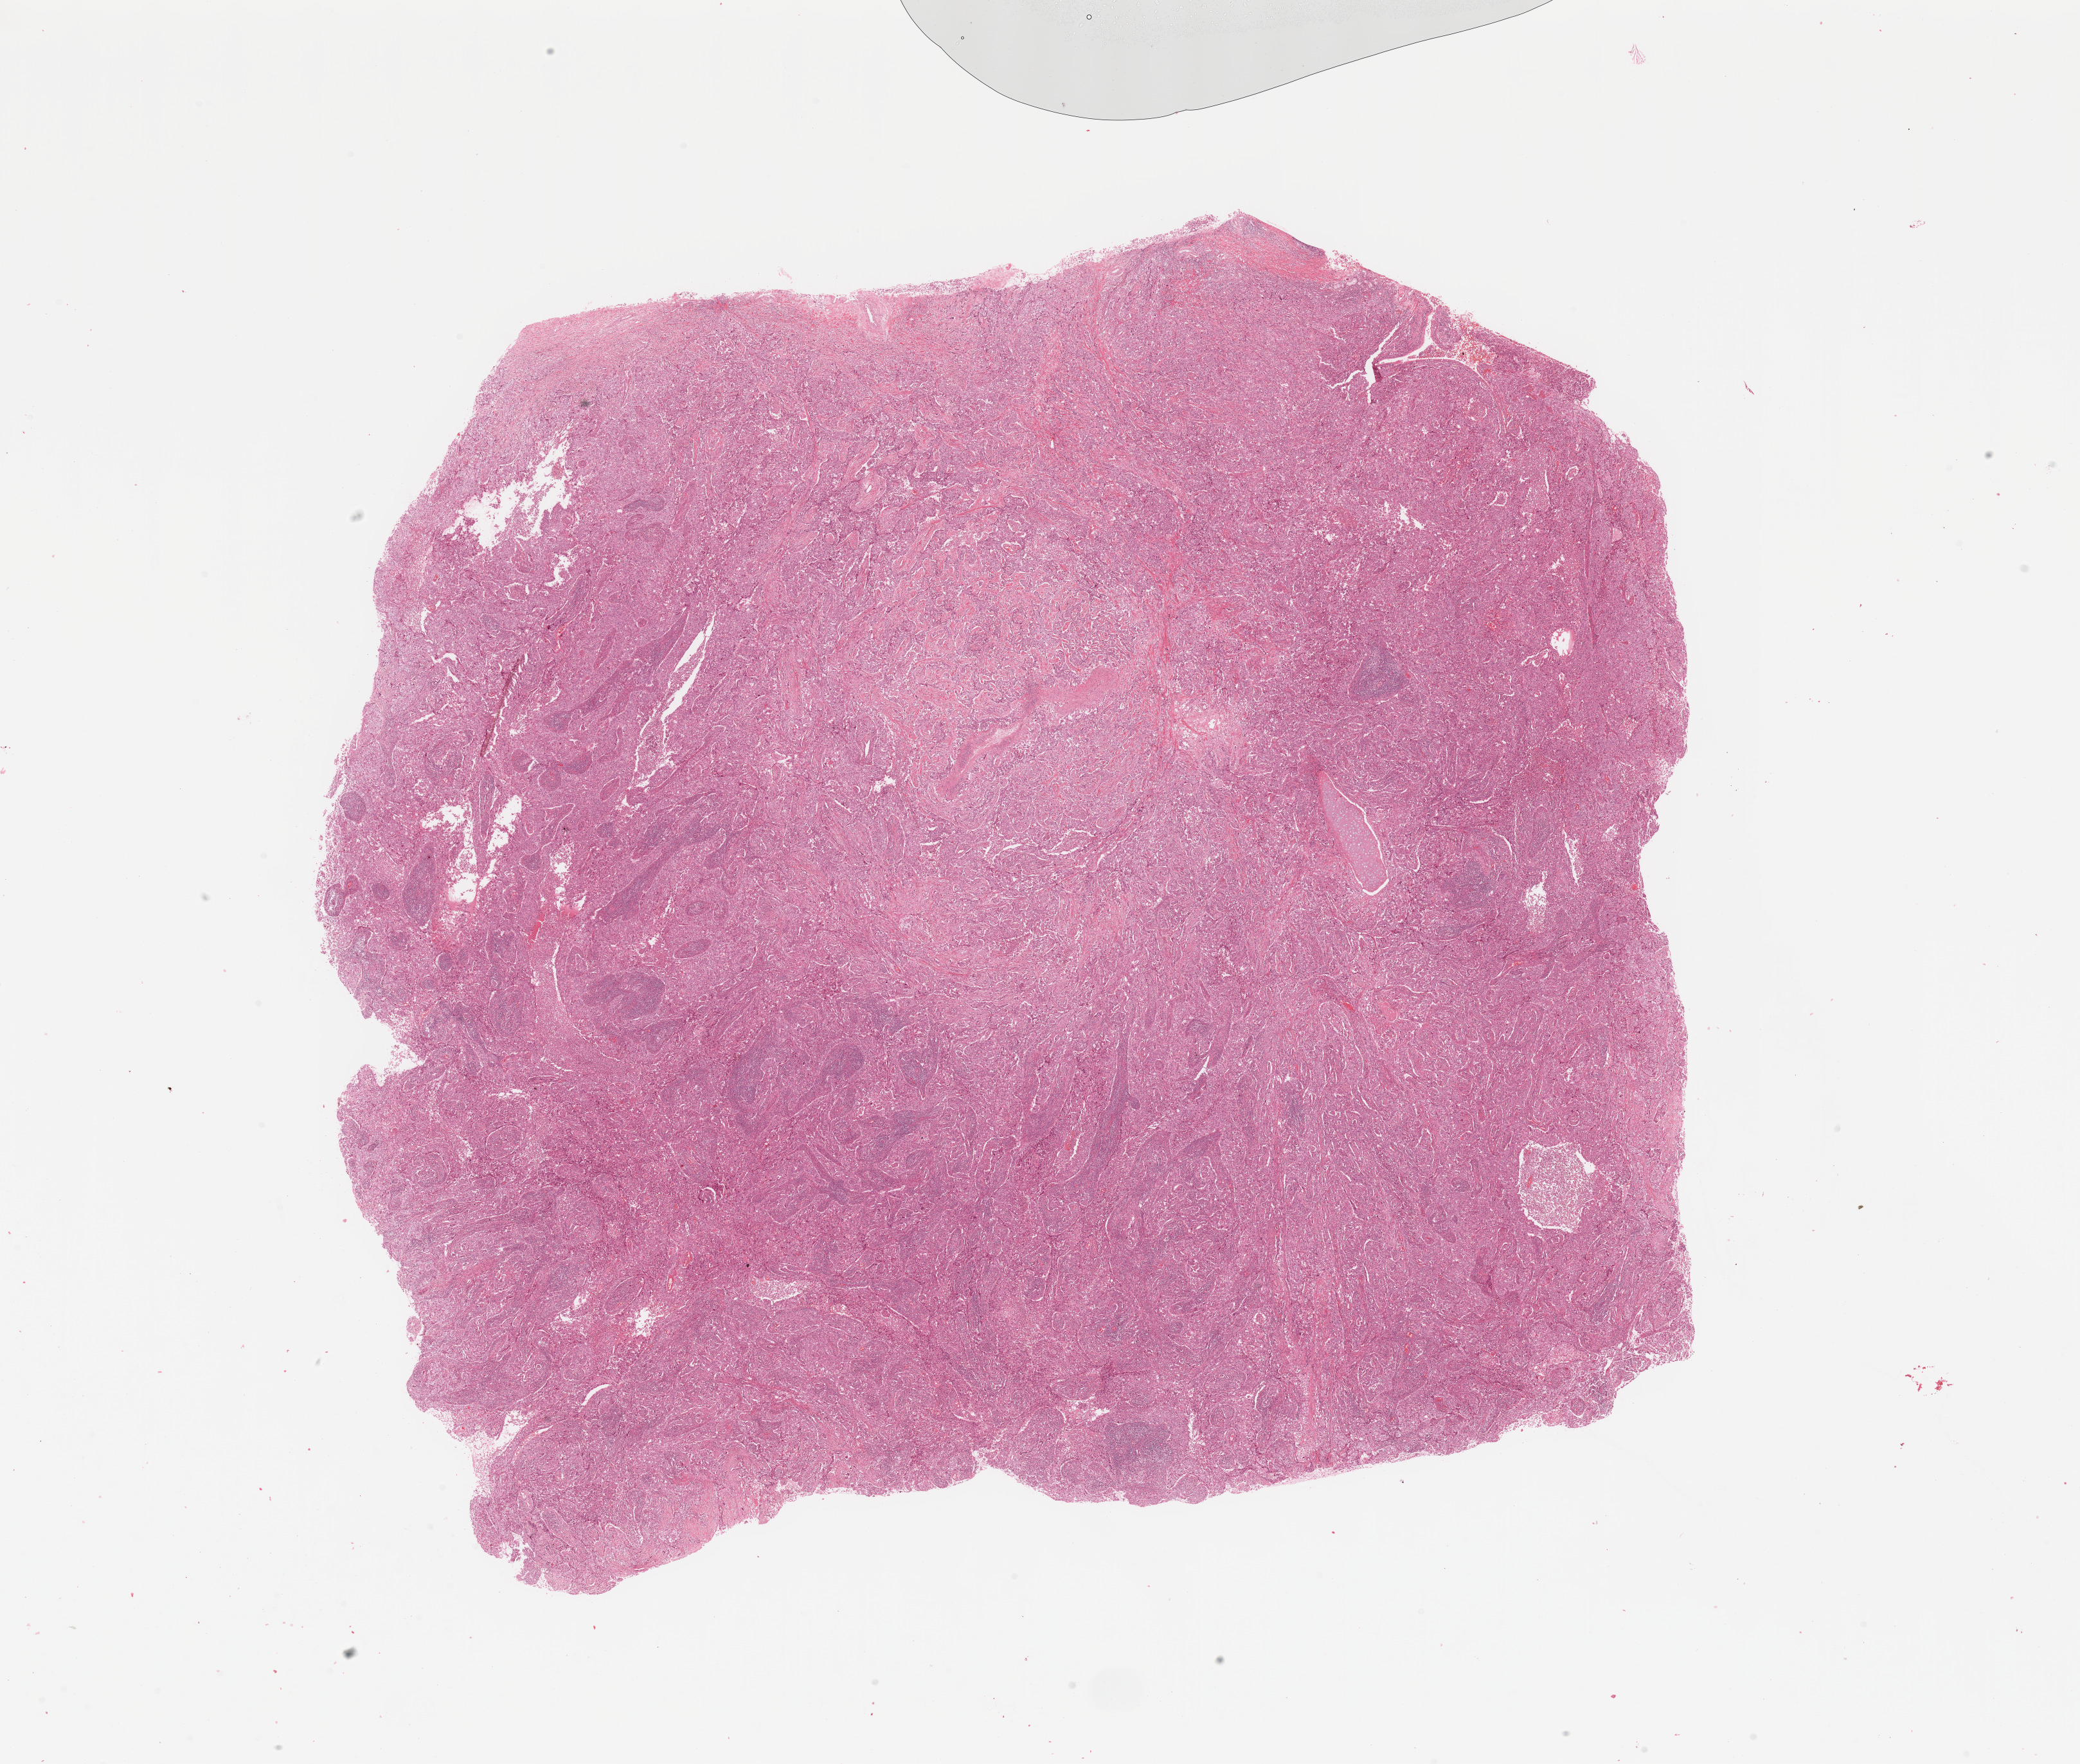
Digitized H&E-stained tissue section (whole slide), a low-resolution overview of the entire scanned area, about 25.6 x 21.7 mm (slide scanned at 20x); tumour tissue sample, lung. Patient: male, age 60 years. Histologic grade: G3 (poorly differentiated).
* histologic diagnosis: Adenocarcinoma, NOS
* AJCC pathologic stage: IIB